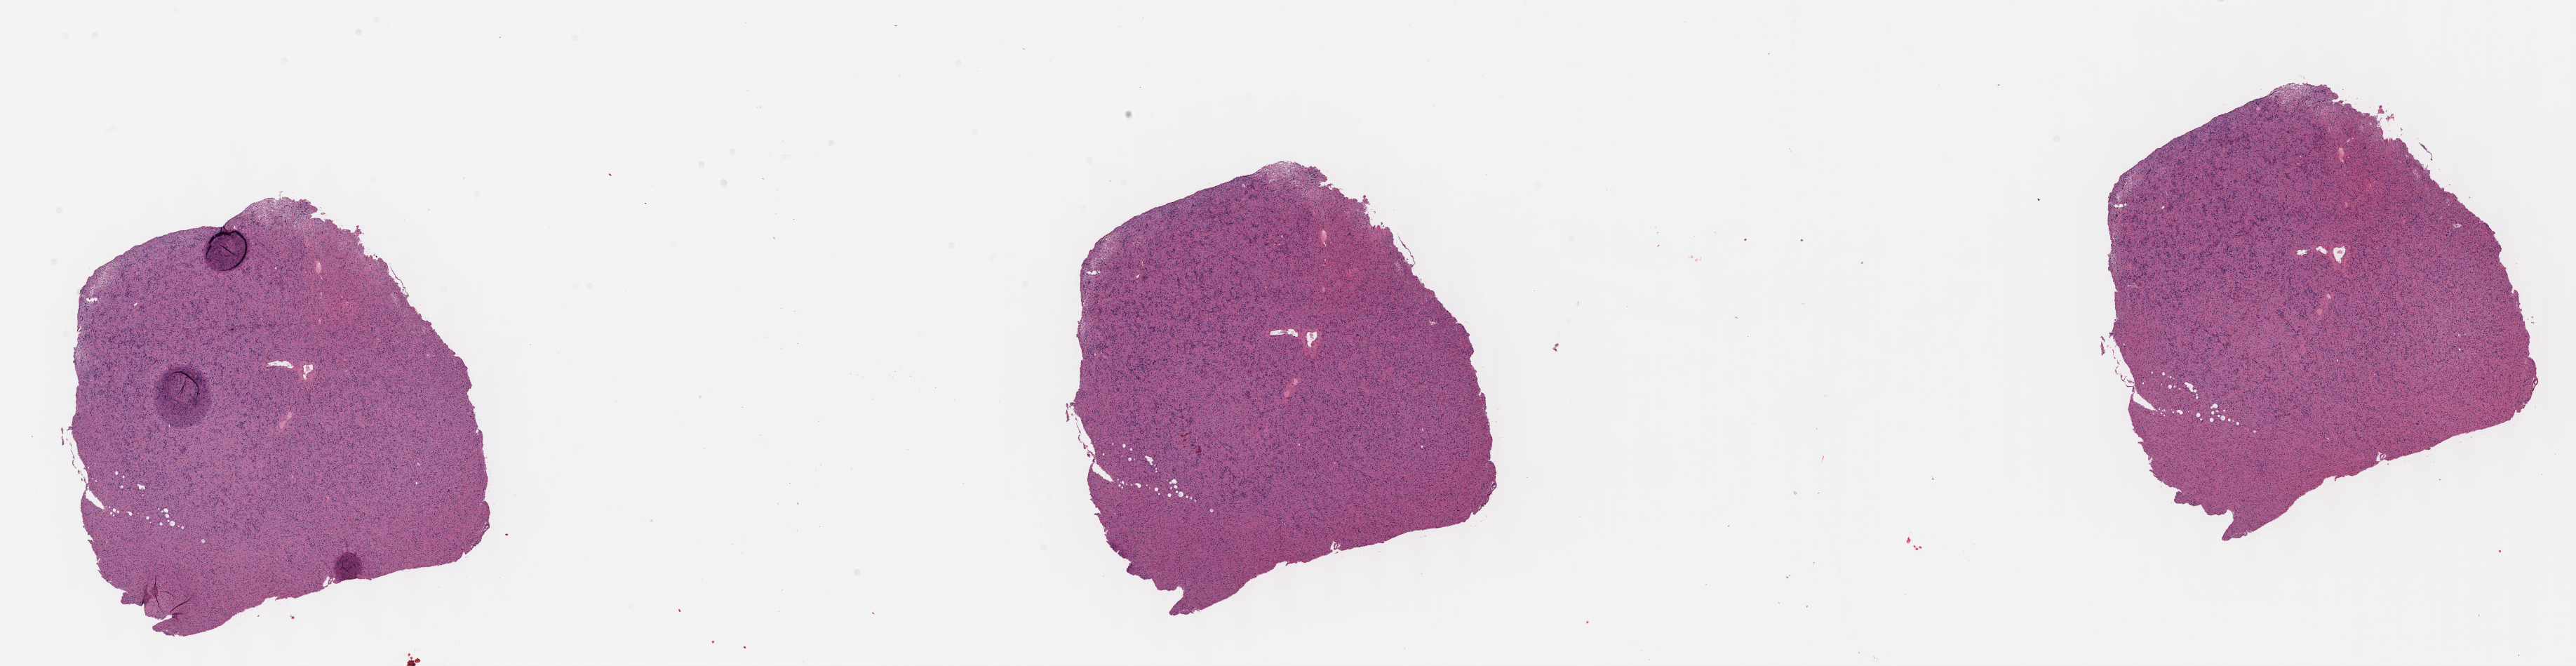
H&E whole-slide image, a low-resolution overview of the entire scanned area, about 29.7 x 7.7 mm (from a 40x scan); FFPE section; brain, primary tumour sample. Female patient; age at initial diagnosis 33 years.
Pathologic diagnosis: Astrocytoma, anaplastic (cerebrum).